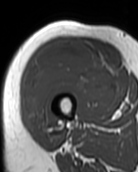
MRI of an extremity soft-tissue mass, one axial slice; MR volume resampled by the dataset authors to the PET/CT grid (not the native acquisition matrix); 138 × 172 image matrix, field of view 135 × 168 mm. Female patient. From the clinical record (not read from this slice): histological type: pleiomorphic undifferentiated sarcoma; grade: high; site of the primary tumour: right quadricep.
Annotated regions visible in this slice (expert contour drawn on MRI and transferred to this co-registered scan by the dataset authors):
- gross tumour volume including surrounding oedema: bounding box (x1, y1, x2, y2) in pixels: (25, 43, 111, 128)
- gross tumour volume (mass): (25, 43, 111, 128)